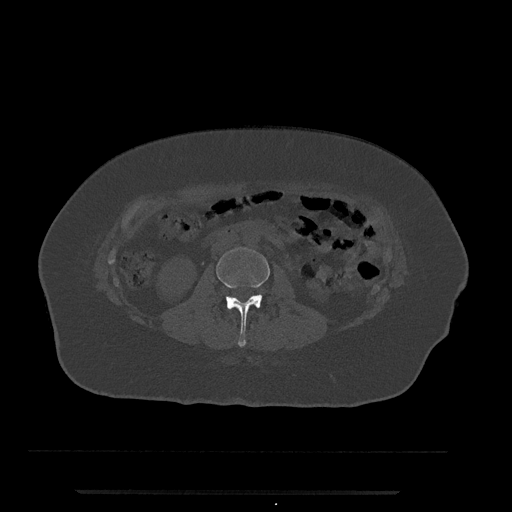
CT including the spine, one axial slice; slice 27 of 797 in the series (ordered by position); 120 kVp; bone window (W 1800 / L 400 HU); 512 × 512 image matrix, field of view 440 × 440 mm. Patient: female, 51 years. From the clinical record (not read from this slice): primary cancer: neuro; vertebrae with lytic lesions (as recorded): T8.
Structures marked on this image (semi-automatic segmentation, software-assisted and operator-edited):
- L2 vertebra: bounding box (x1, y1, x2, y2) in pixels: (216, 247, 270, 347)